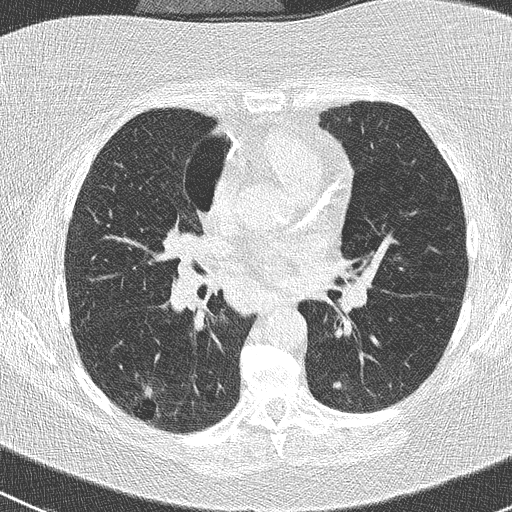
Low-dose screening chest CT, one axial slice; position 137 of 261 along the scan axis; reconstruction kernel B50f; lung window (W 1500 / L -600 HU); 512 × 512 image matrix, field of view 310 × 310 mm.
Structures marked on this image (manually delineated by an expert):
- lesion 1 (tumor, lower lobe of right lung): box from (x=144, y=386) to (x=153, y=398) px